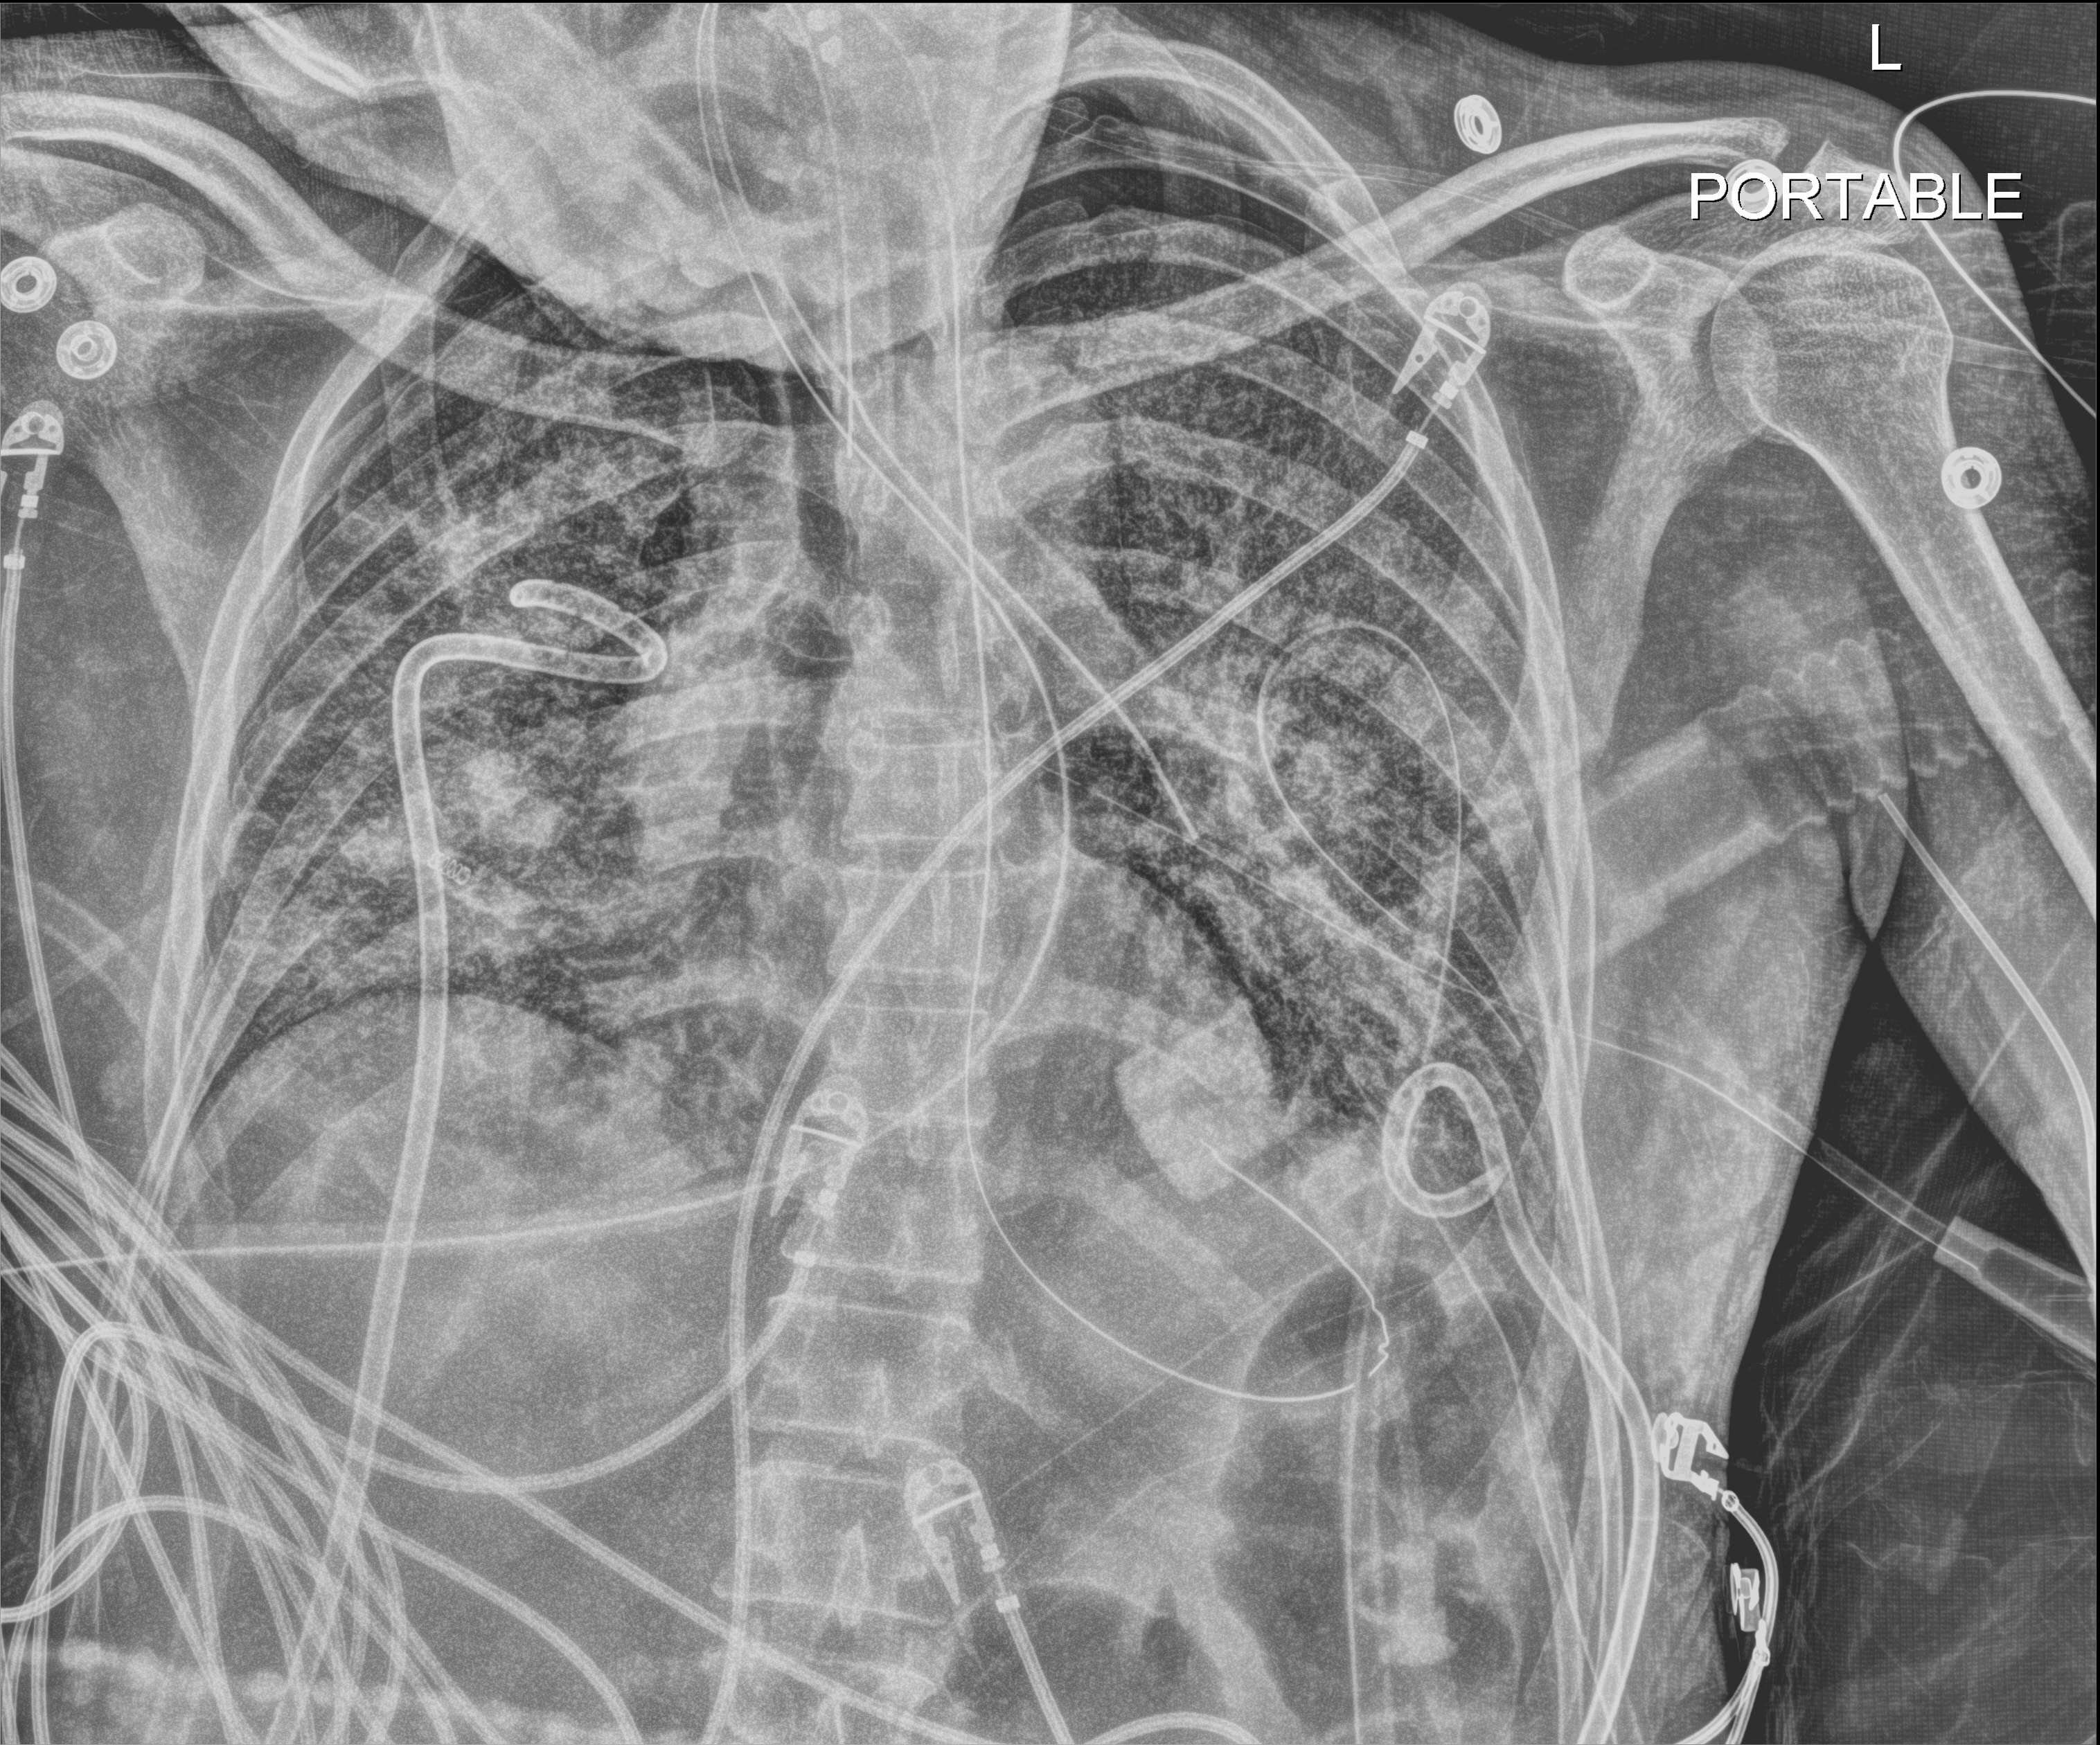
Portable chest radiograph, anteroposterior (AP) projection. Patient hospitalised with COVID-19, aged 18–59 years.
Hospital-stay facts (about this admission, not read from this image; timing relative to this image not recorded):
- hypertension (admission record): no
- length of hospital stay: 41 days
- mechanically ventilated during this hospital stay: yes